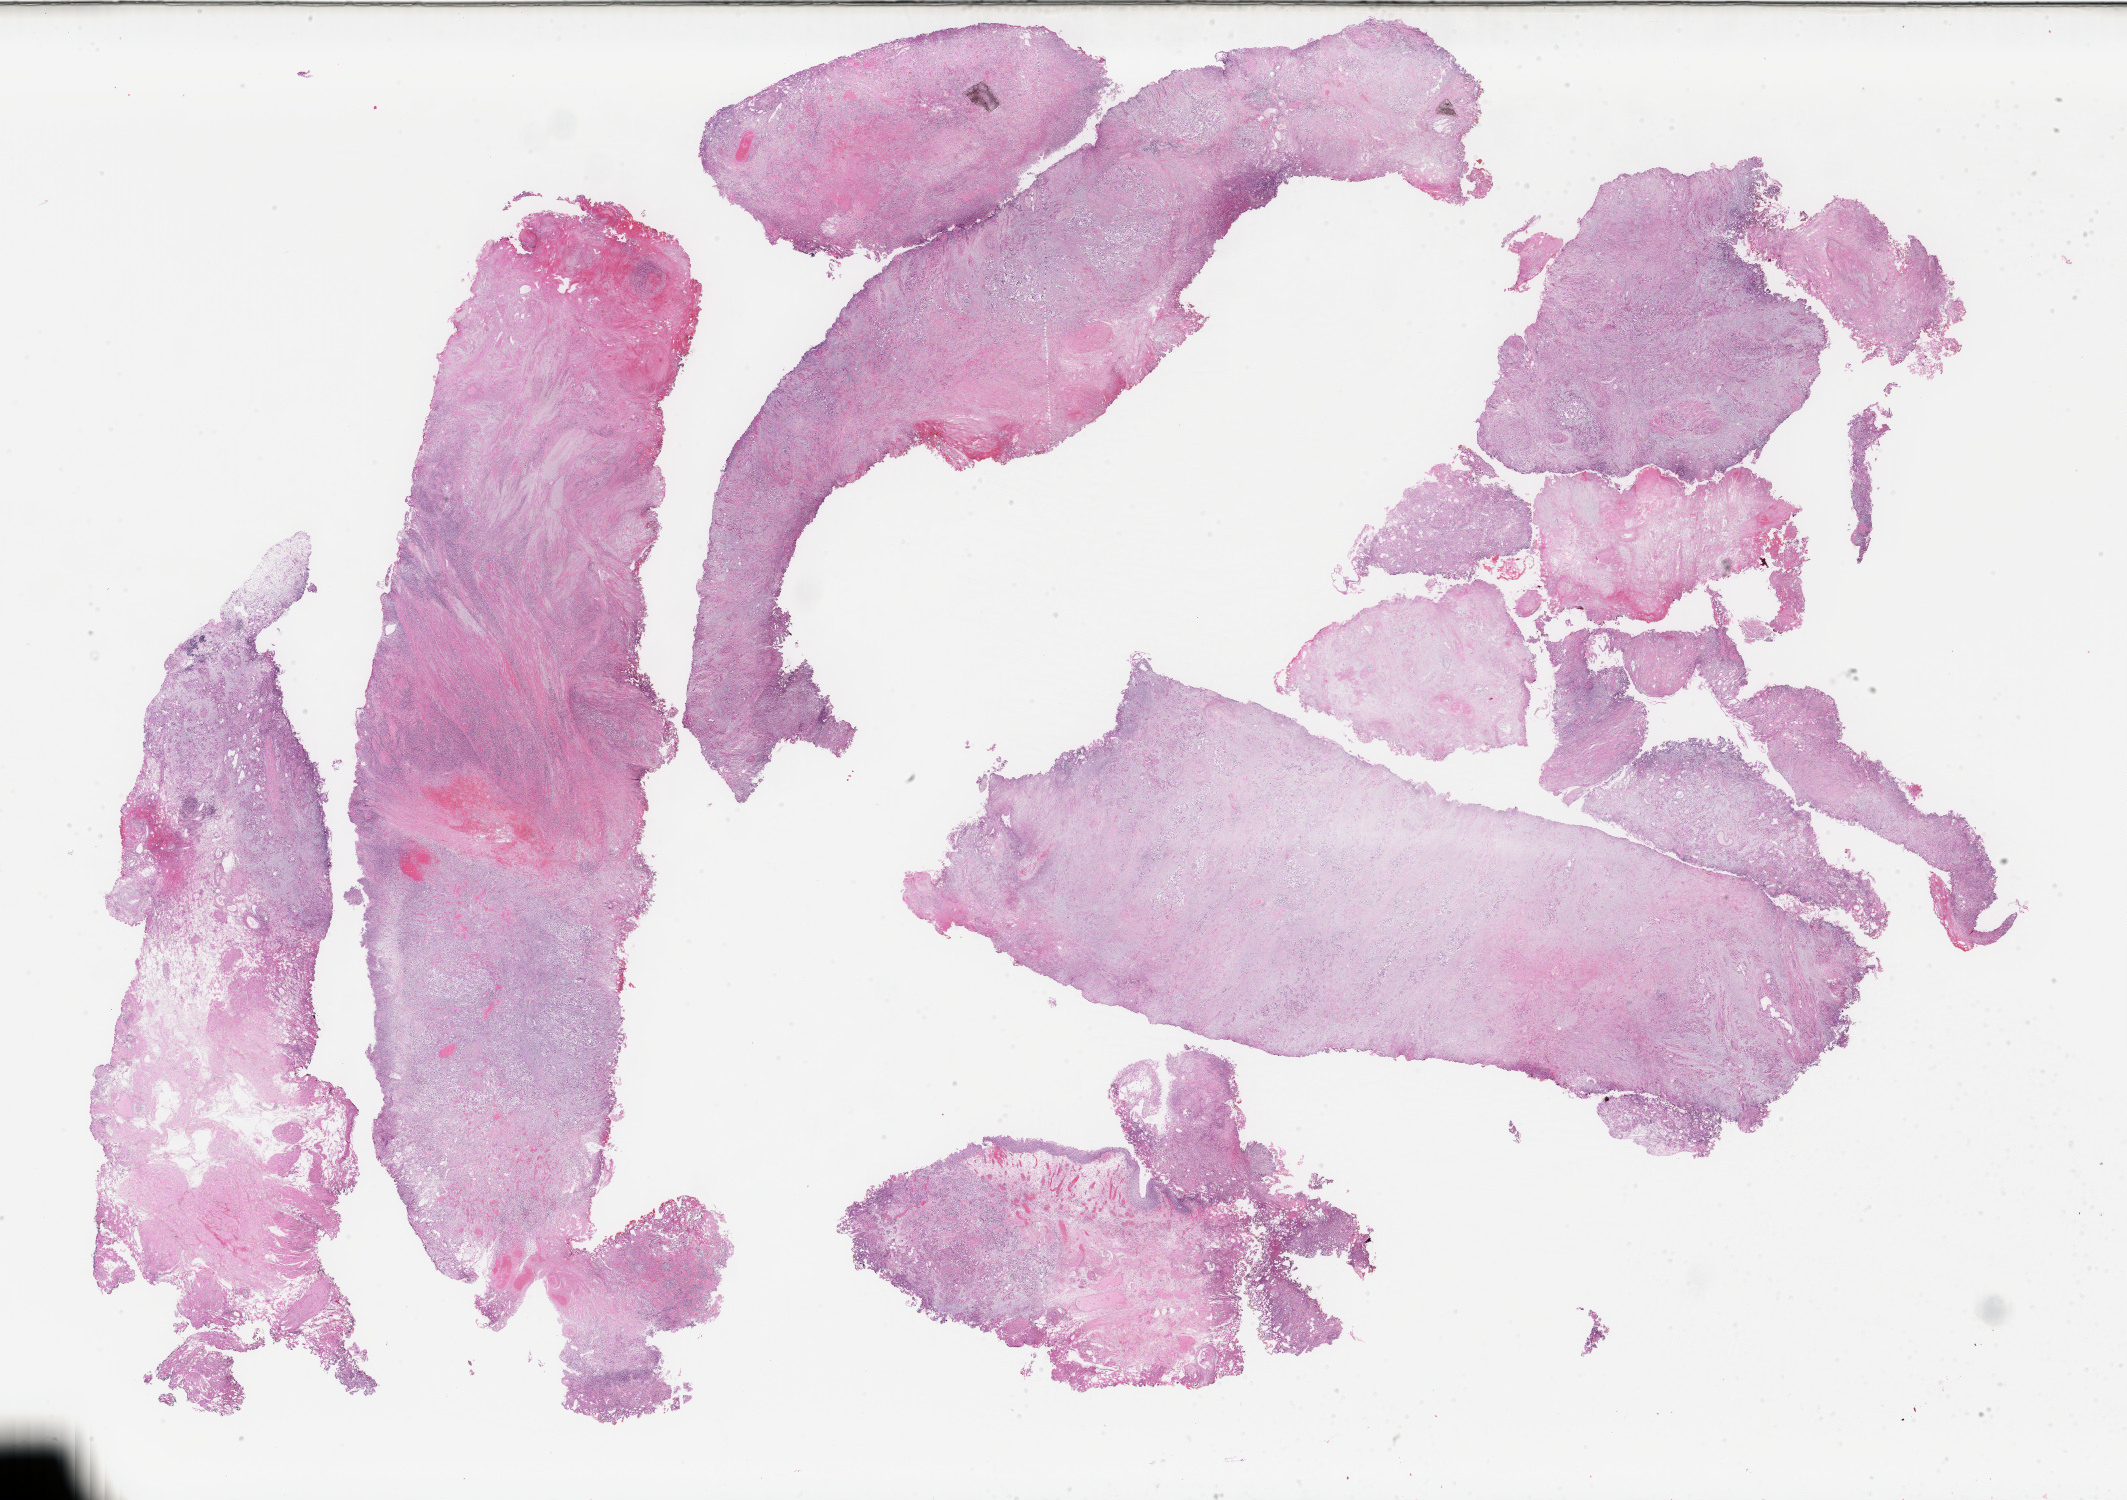
Digitized H&E tissue section (whole slide) — low-resolution overview of the scanned area, about 33.8 x 23.8 mm; FFPE section; primary tumour sample from the bladder. Female, age 58 years at initial diagnosis.
Histologic diagnosis: Transitional cell carcinoma.